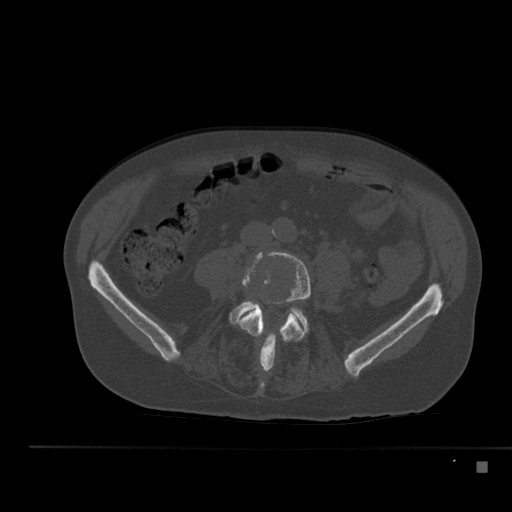
CT including the spine, one axial slice. Slice 137 of 517 in the series (ordered by position). 120 kVp. Bone window (W 1800 / L 400 HU). 1.5 mm slice thickness. 512 × 512 image matrix, field of view 408 × 408 mm. Male patient, age 70 years. Case-level facts recorded for this patient, not image findings: primary cancer: renal; vertebrae with lytic lesions (as recorded): T4, T6, T10, T12, L3, L4, L5.
Structures marked on this image (semi-automatically segmented with operator editing):
- L4 vertebra: bounding box <238,251,311,372> (left, top, right, bottom; pixels)
- L5 vertebra: <230,301,308,357>